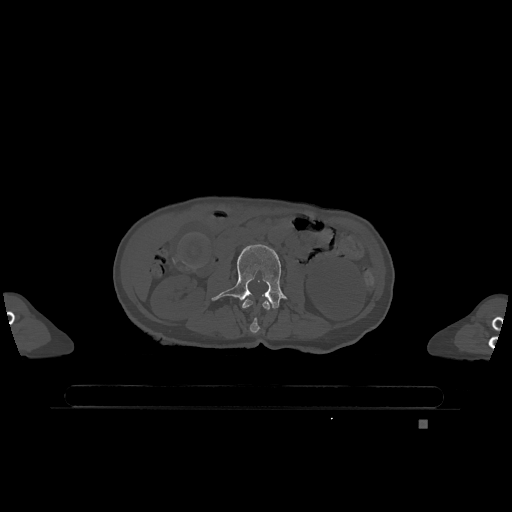
CT including the spine, one axial slice. Slice 369 of 1317 in the series (ordered by position). Bone window (W 1800 / L 400 HU). 0.5 mm slice thickness. 512 × 512 image matrix. Female patient, age 74 years. Case-level facts recorded for this patient, not image findings: primary cancer: lung; vertebrae with lytic lesions (as recorded): T1, T4, T5, T6, L4, L5.
Structures marked on this image (semi-automatic segmentation, software-assisted and operator-edited):
- L2 vertebra: bounding box <242,299,271,334> (left, top, right, bottom; pixels)
- L3 vertebra: <212,244,286,309>